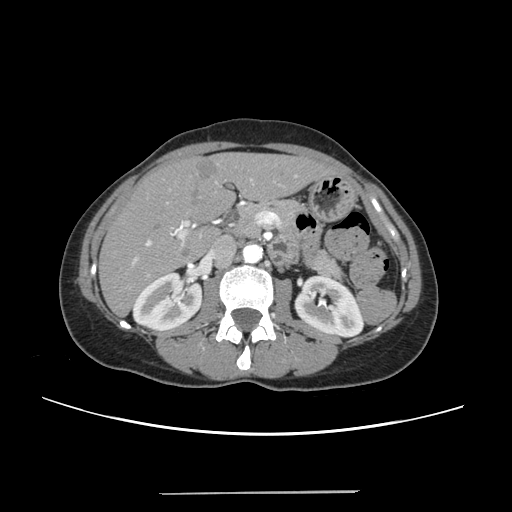
Contrast-enhanced abdominal CT, one axial slice. Slice 120 of 240 in the series (ordered by position). Intravenous contrast given. Soft-tissue window (W 400 / L 40 HU). 1.25 mm slice thickness. 512 × 512 image matrix. Female patient, age 60 years. Case-level facts recorded for this patient, not image findings: diagnosis: colorectal cancer liver metastases, imaged before liver resection; multiple liver metastases: no; largest metastasis: 1.5 cm; disease in both lobes: no.
Structures marked on this image (outlined manually by an expert reader):
- liver: bounding box (x1, y1, x2, y2) in pixels: (101, 153, 329, 314)
- planned liver remnant (the part of the liver to remain after resection): (101, 154, 329, 313)
- portal vein (with intrahepatic branches): (132, 175, 296, 276)
- liver metastasis: (195, 160, 218, 181)